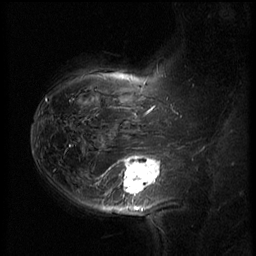
Breast MRI (dynamic contrast-enhanced), one sagittal slice; slice 46 of 62 in the series (ordered by position); 3 images stored at this slice position (order not interpretable as contrast timing); 1.5 T; TE 4.2 ms, TR 8.9 ms; 2.5 mm slice thickness; 256 × 256 image matrix. Female patient, age 37 years. From the clinical record (not read from this slice): setting: breast cancer imaged before/during neoadjuvant chemotherapy; receptor status: triple-negative.
Outlined on this slice (semi-automatic segmentation, software-assisted and operator-edited):
- analysis volume of interest (the breast-tissue region the enhancement analysis was run in; not a lesion): box from (x=116, y=146) to (x=168, y=203) px
- tumour enhancement mask (voxels above the 140 % enhancement threshold inside the analysis volume of interest): (x=122, y=156)–(x=160, y=194)